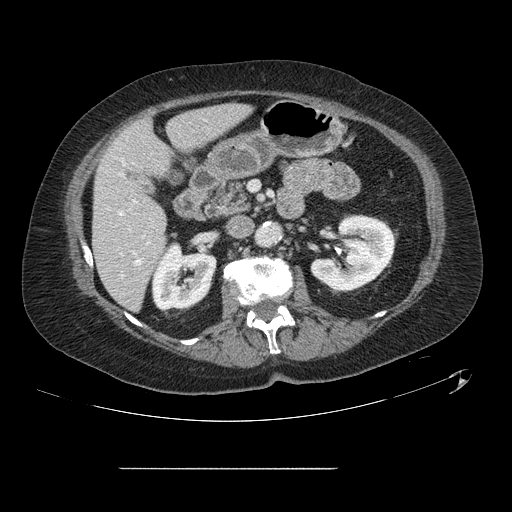
Contrast-enhanced abdominal CT, one axial slice; position 51 of 148 along the scan axis; 120 kVp; soft-tissue window (W 400 / L 40 HU); 2.5 mm slice thickness; 512 × 512 image matrix, field of view 439 × 439 mm. Female patient, age 75 years. From the clinical record (not read from this slice): diagnosis: colorectal cancer liver metastases, imaged before liver resection; multiple liver metastases: no; largest metastasis: 2.4 cm; disease in both lobes: no.
Structures marked on this image (outlined manually by an expert reader):
- hepatic veins: bounding box [x1, y1, x2, y2] px = [119, 212, 141, 264]
- liver: [94, 103, 249, 309]
- planned liver remnant (the part of the liver to remain after resection): [94, 103, 250, 309]